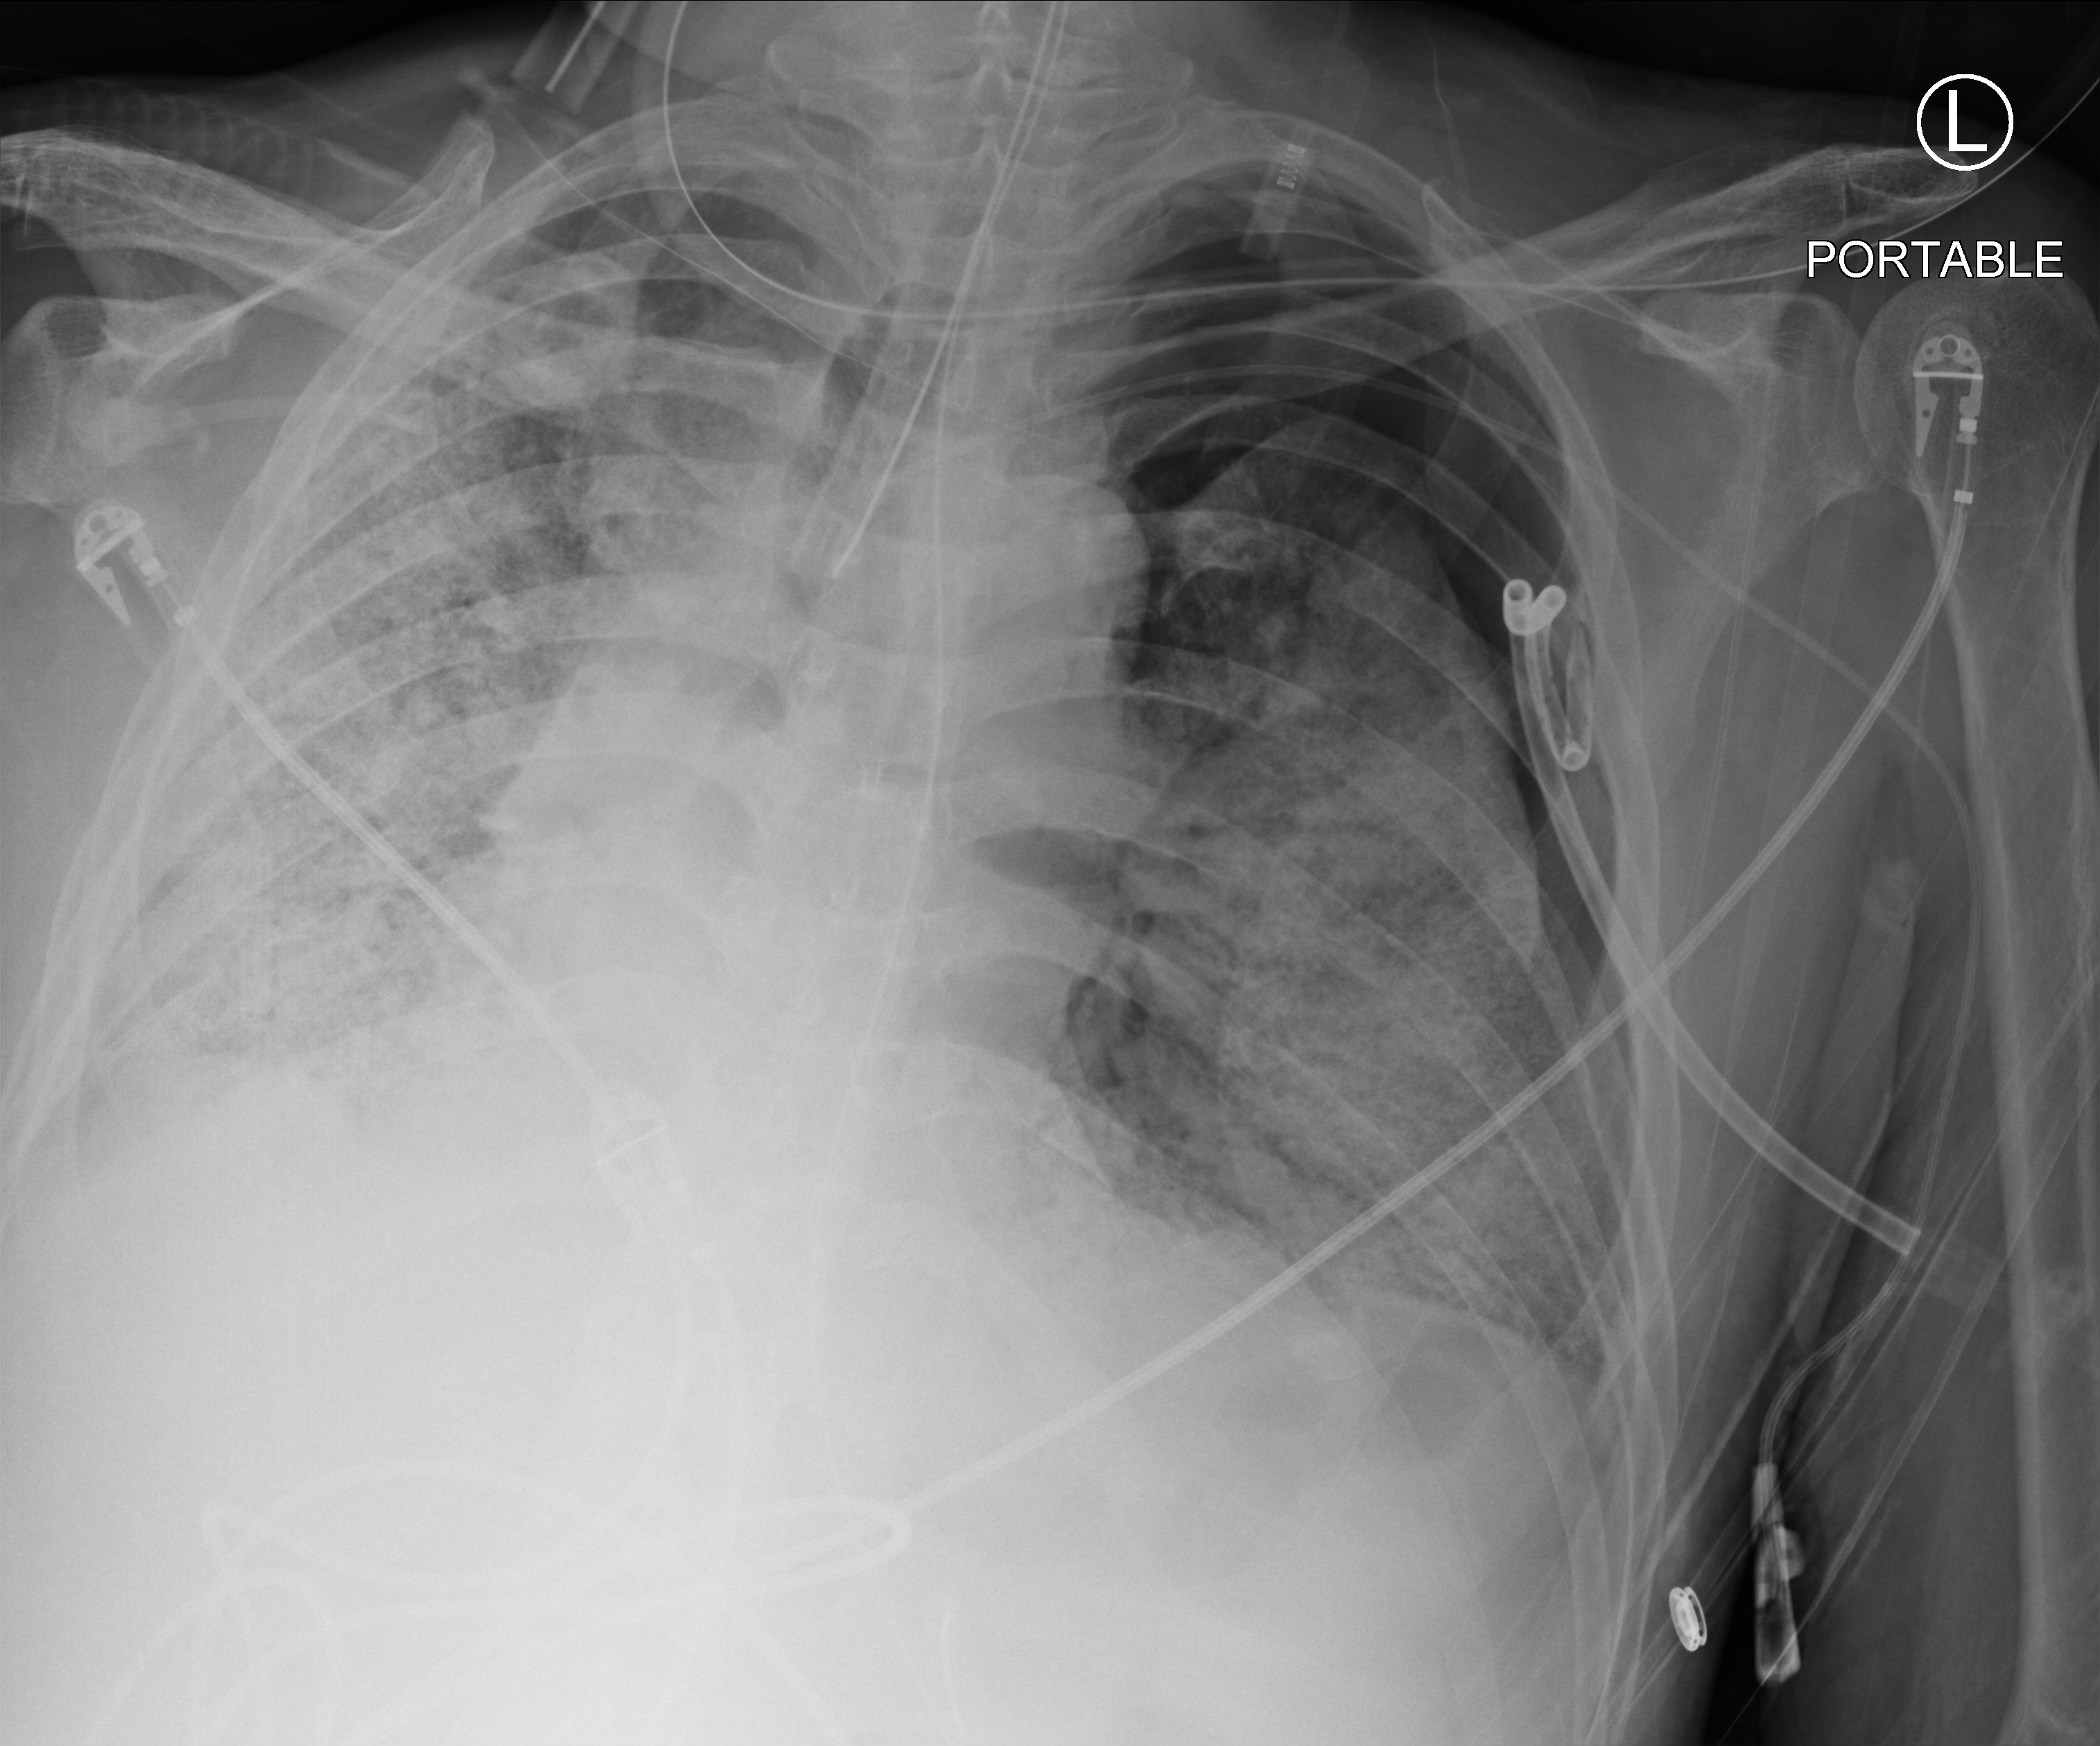
Portable chest radiograph; anteroposterior (AP) projection. Male patient hospitalised with COVID-19, age 60–74 years.
From the hospital-stay record, not from the radiograph (when in the stay this image was taken is not recorded): mechanically ventilated during this hospital stay: yes; admitted to intensive care during this hospital stay: yes; length of hospital stay: 54 days.